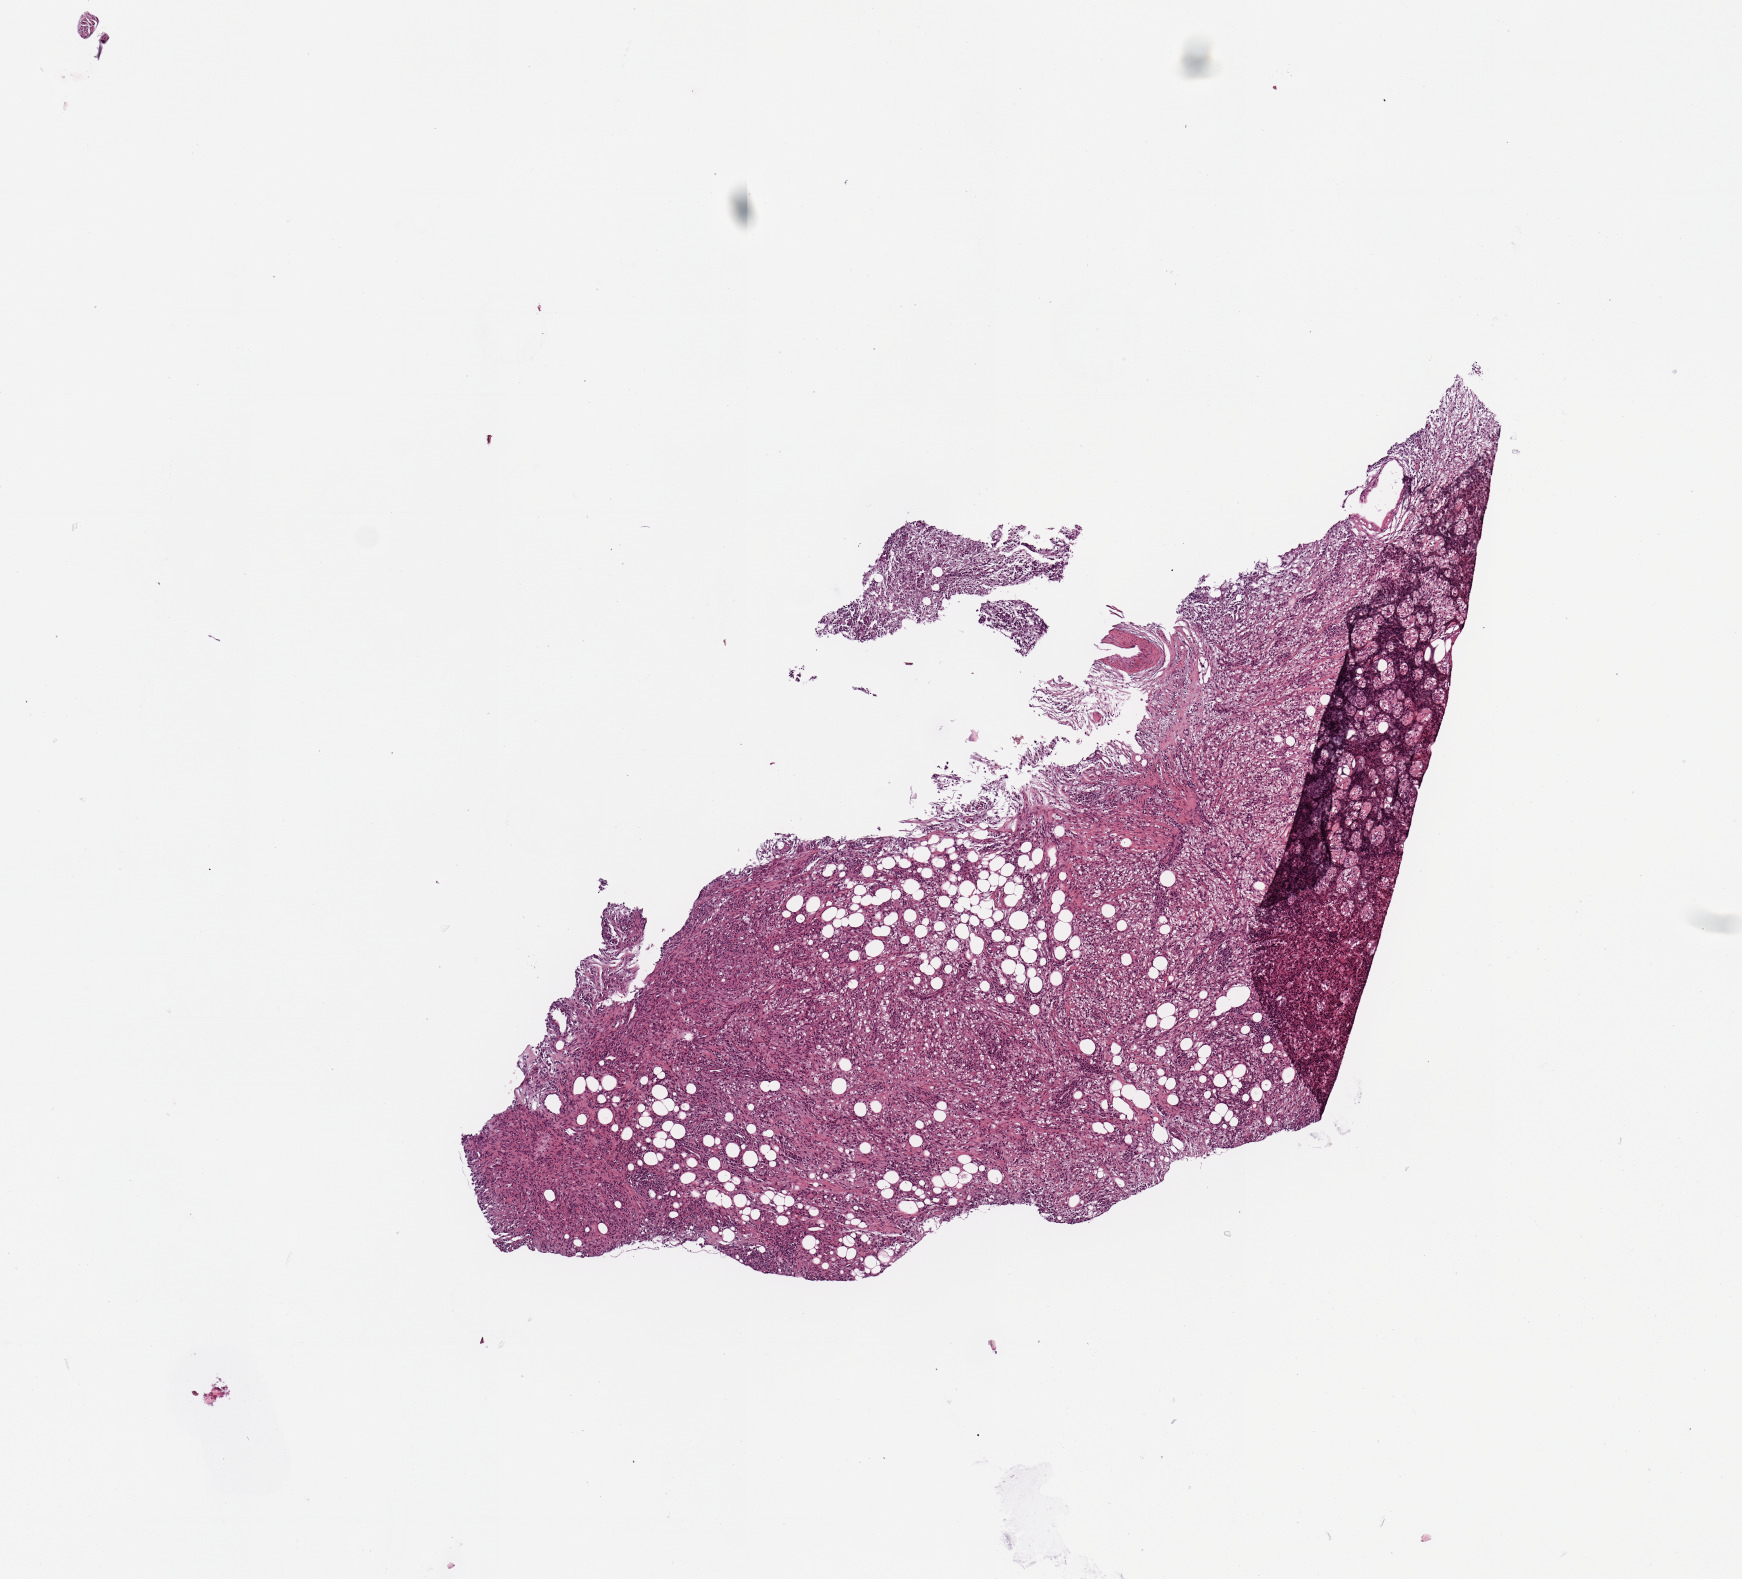
Digitized Hematoxylin and eosin (H&E) stained tissue section (whole slide) — shown as a low-resolution overview of the whole scanned area (about 6.9 x 6.2 mm, acquisition: 20x scan). Tumour tissue sample, sampled site: kidney. 69-year-old male patient. Histologic grade: G2 (moderately differentiated). Slide review estimates, as recorded: tumour nuclei 80%, necrosis 2%.
- primary tumour site (as recorded): middle
- AJCC pathologic stage: II
- histologic diagnosis: Renal cell carcinoma, NOS